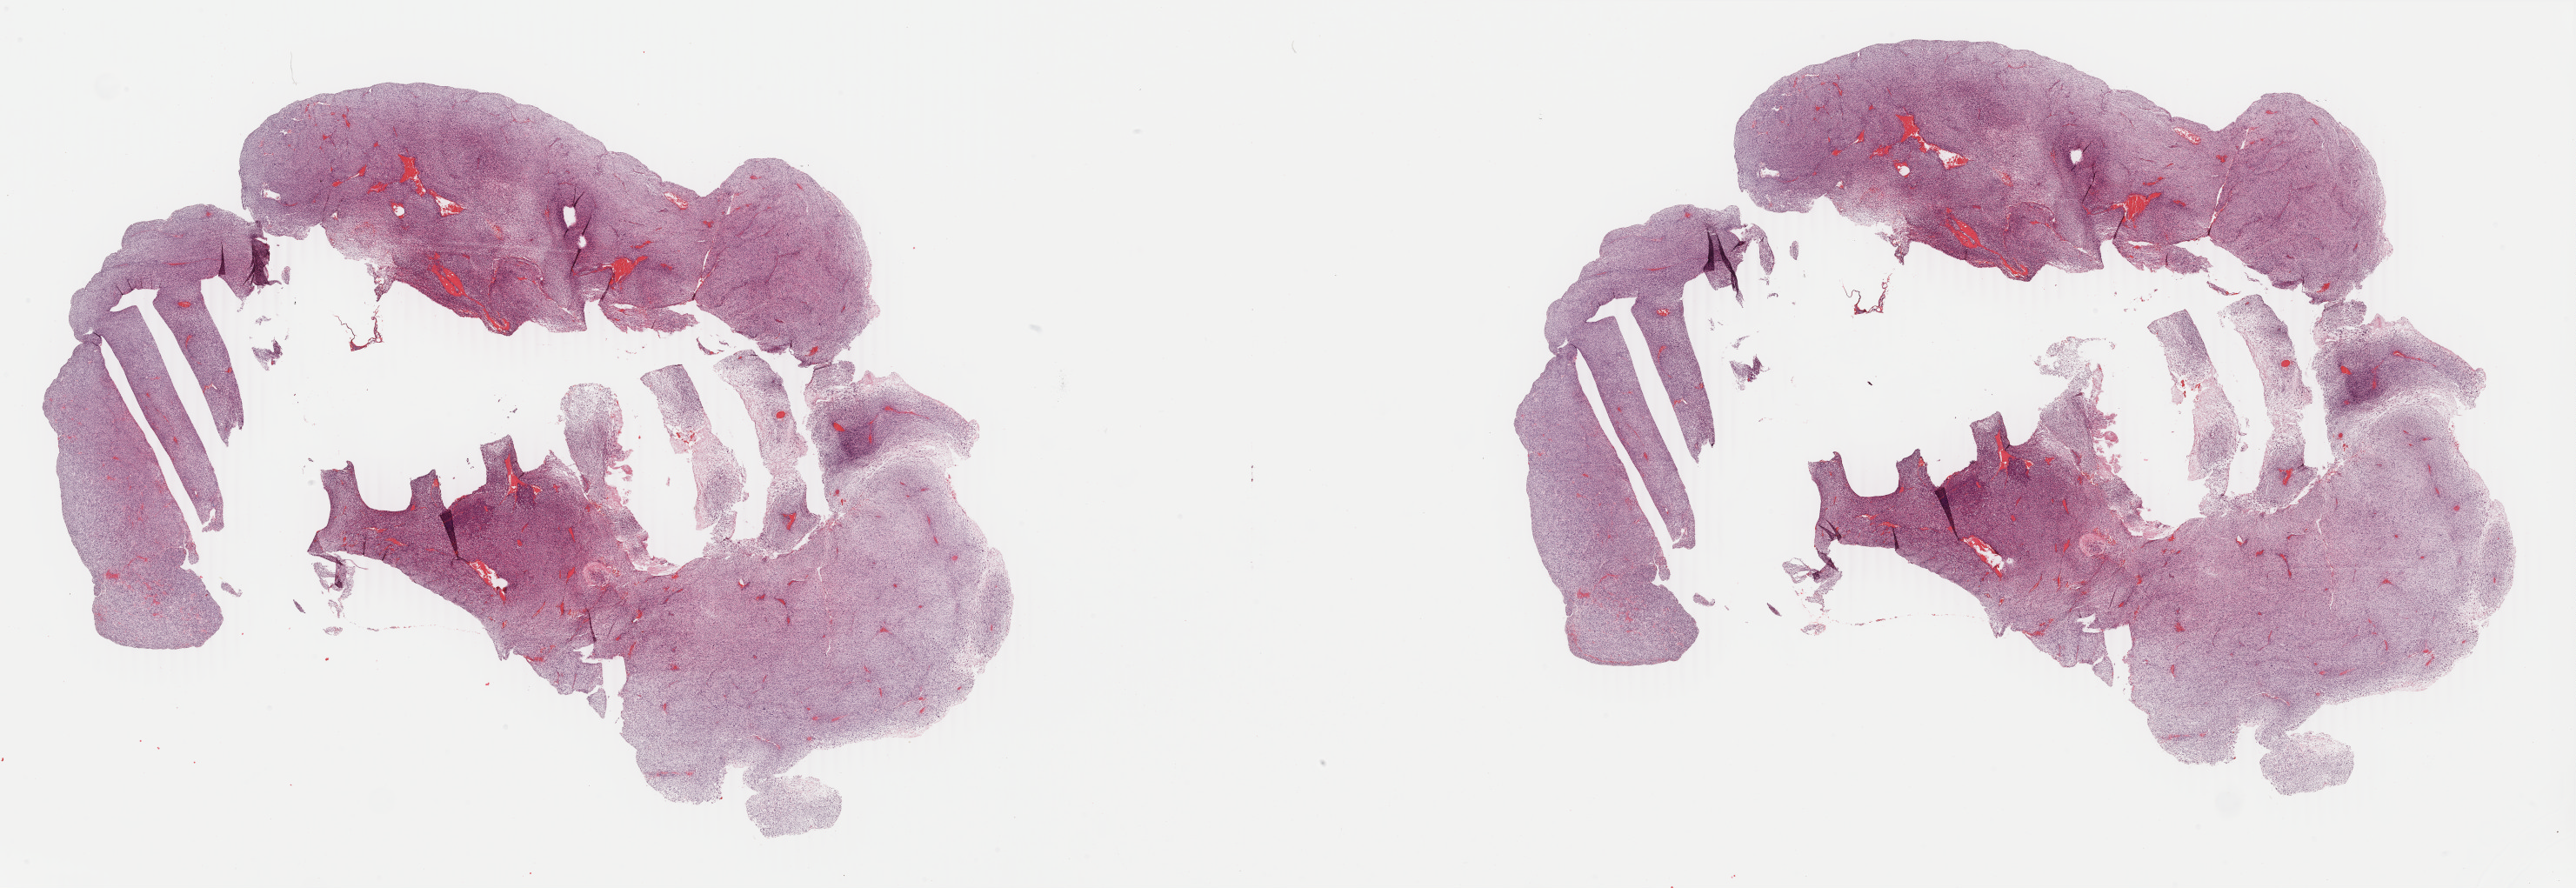
Hematoxylin and eosin (H&E) stained whole-slide image, shown as a low-resolution overview of the whole scanned area (about 47.1 x 16.2 mm, acquisition: 40x scan). FFPE section. Primary tumour sample from the kidney. Patient: male, age at initial diagnosis 75 years.
Pathologic diagnosis: Giant cell sarcoma.